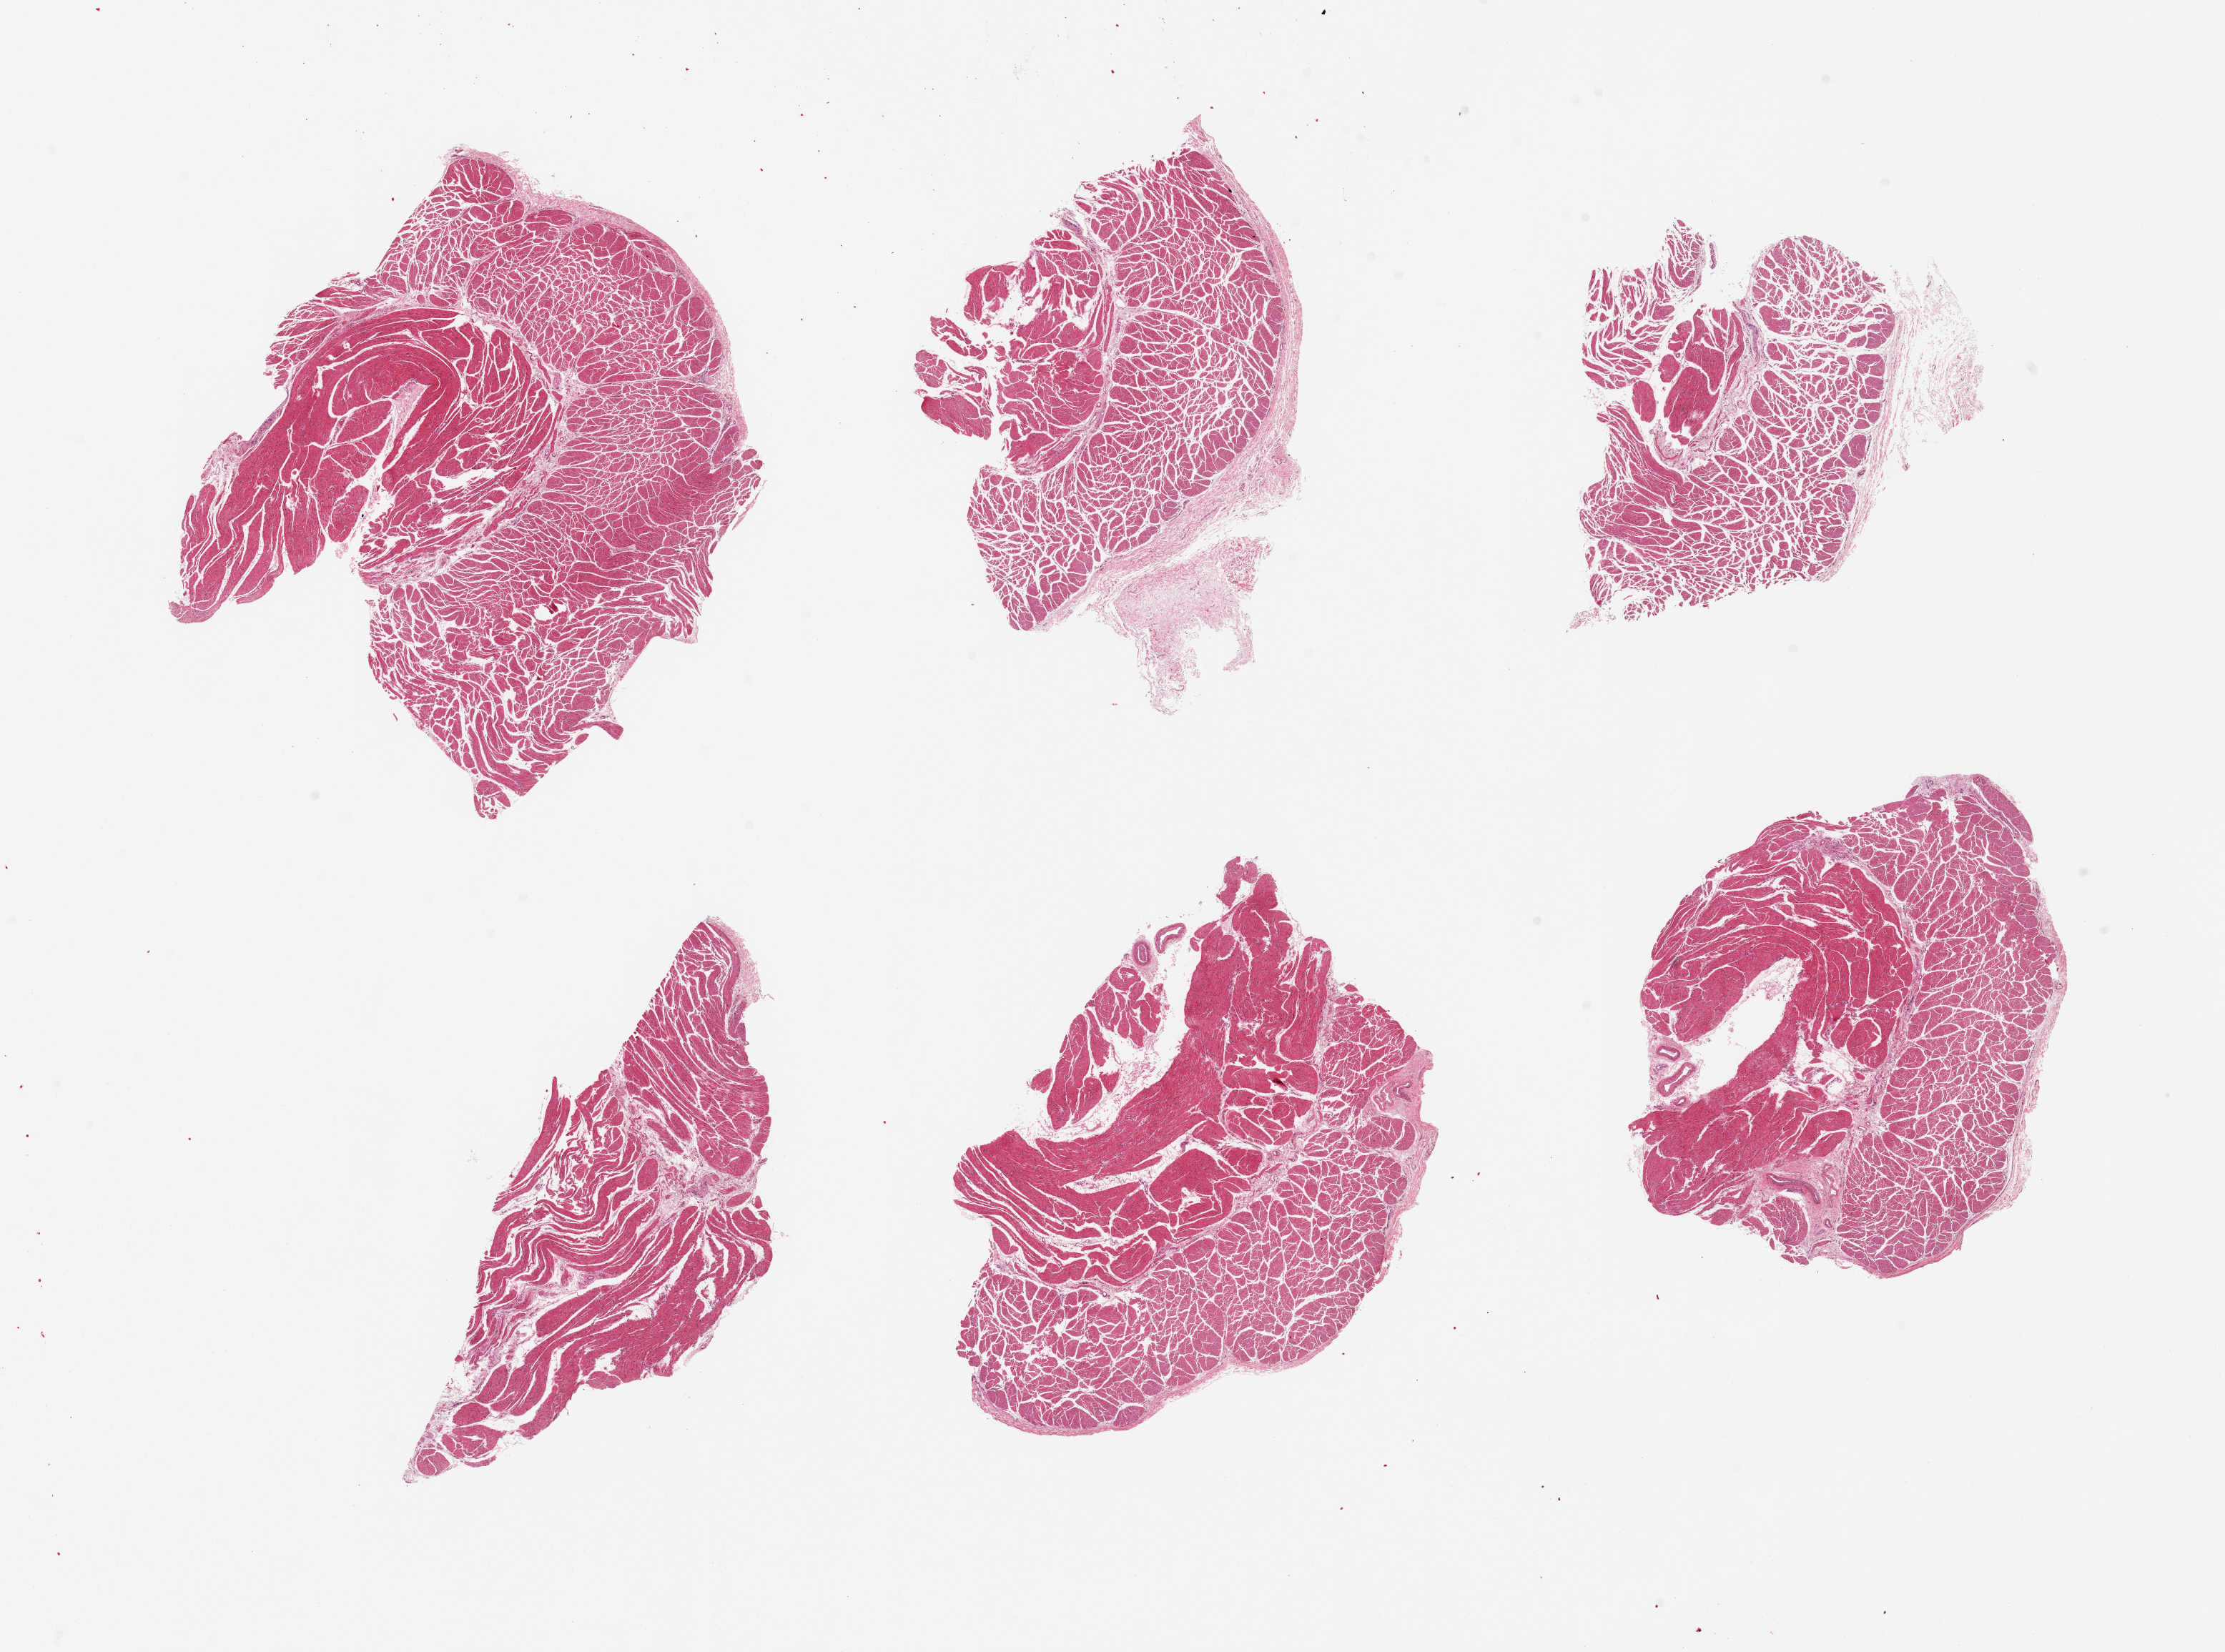
Haematoxylin and eosin whole-slide image, brightfield — whole scanned area (about 24.6 x 18.3 mm, from a 20x scan) shown as a low-resolution overview. PAXgene-fixed, paraffin-embedded tissue. Sampled site (target tissue): esophageal mucous membrane. Tissue donor sample. Female donor.
Pathologist's review note for this sample: 6 pieces; only muscularis propria, no mucosa (target).